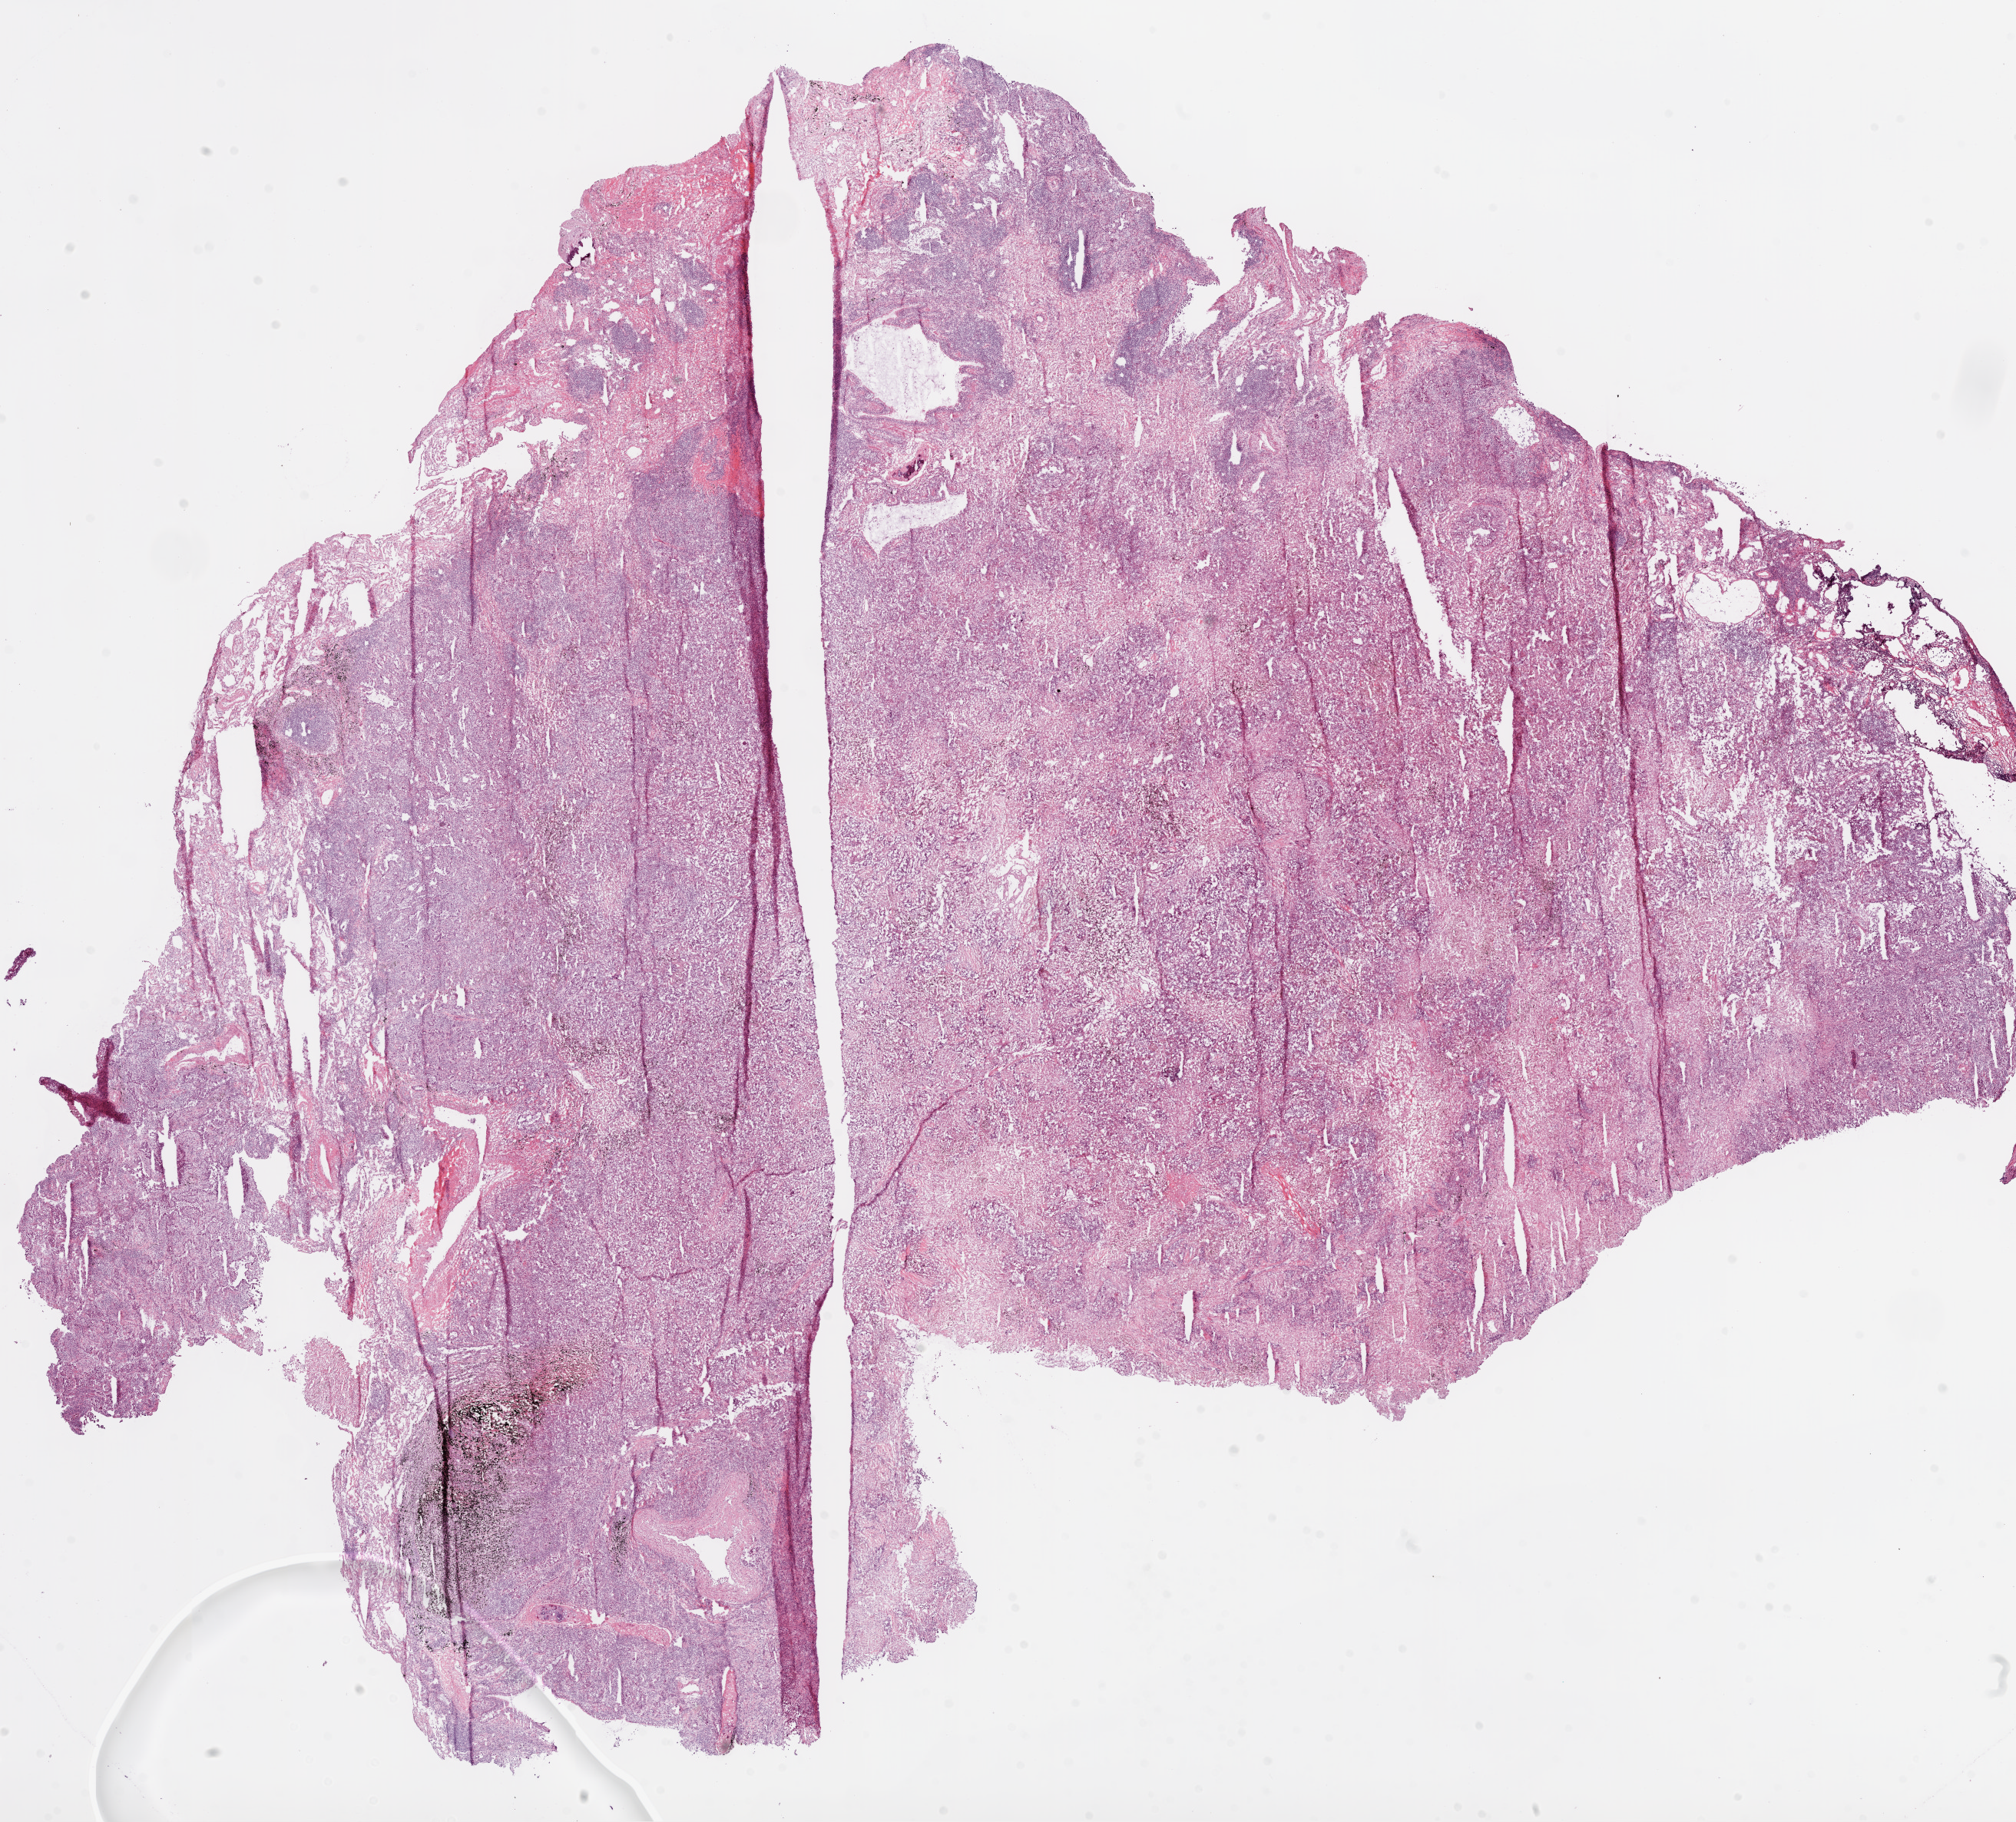
Digitized H&E-stained tissue section (whole slide) — a low-resolution overview of the entire scanned area, about 21.1 x 19.0 mm; frozen section; primary tumour sample from the lung. Patient: male, age at initial diagnosis 70 years. Pathologist review of this section (percent, as recorded): tumour cells 57%, tumour nuclei 65%, normal cells 10%, stromal cells 30%, necrosis 3%.
AJCC pathologic stage: IA (6th edition). Histologic diagnosis: Adenocarcinoma, NOS.